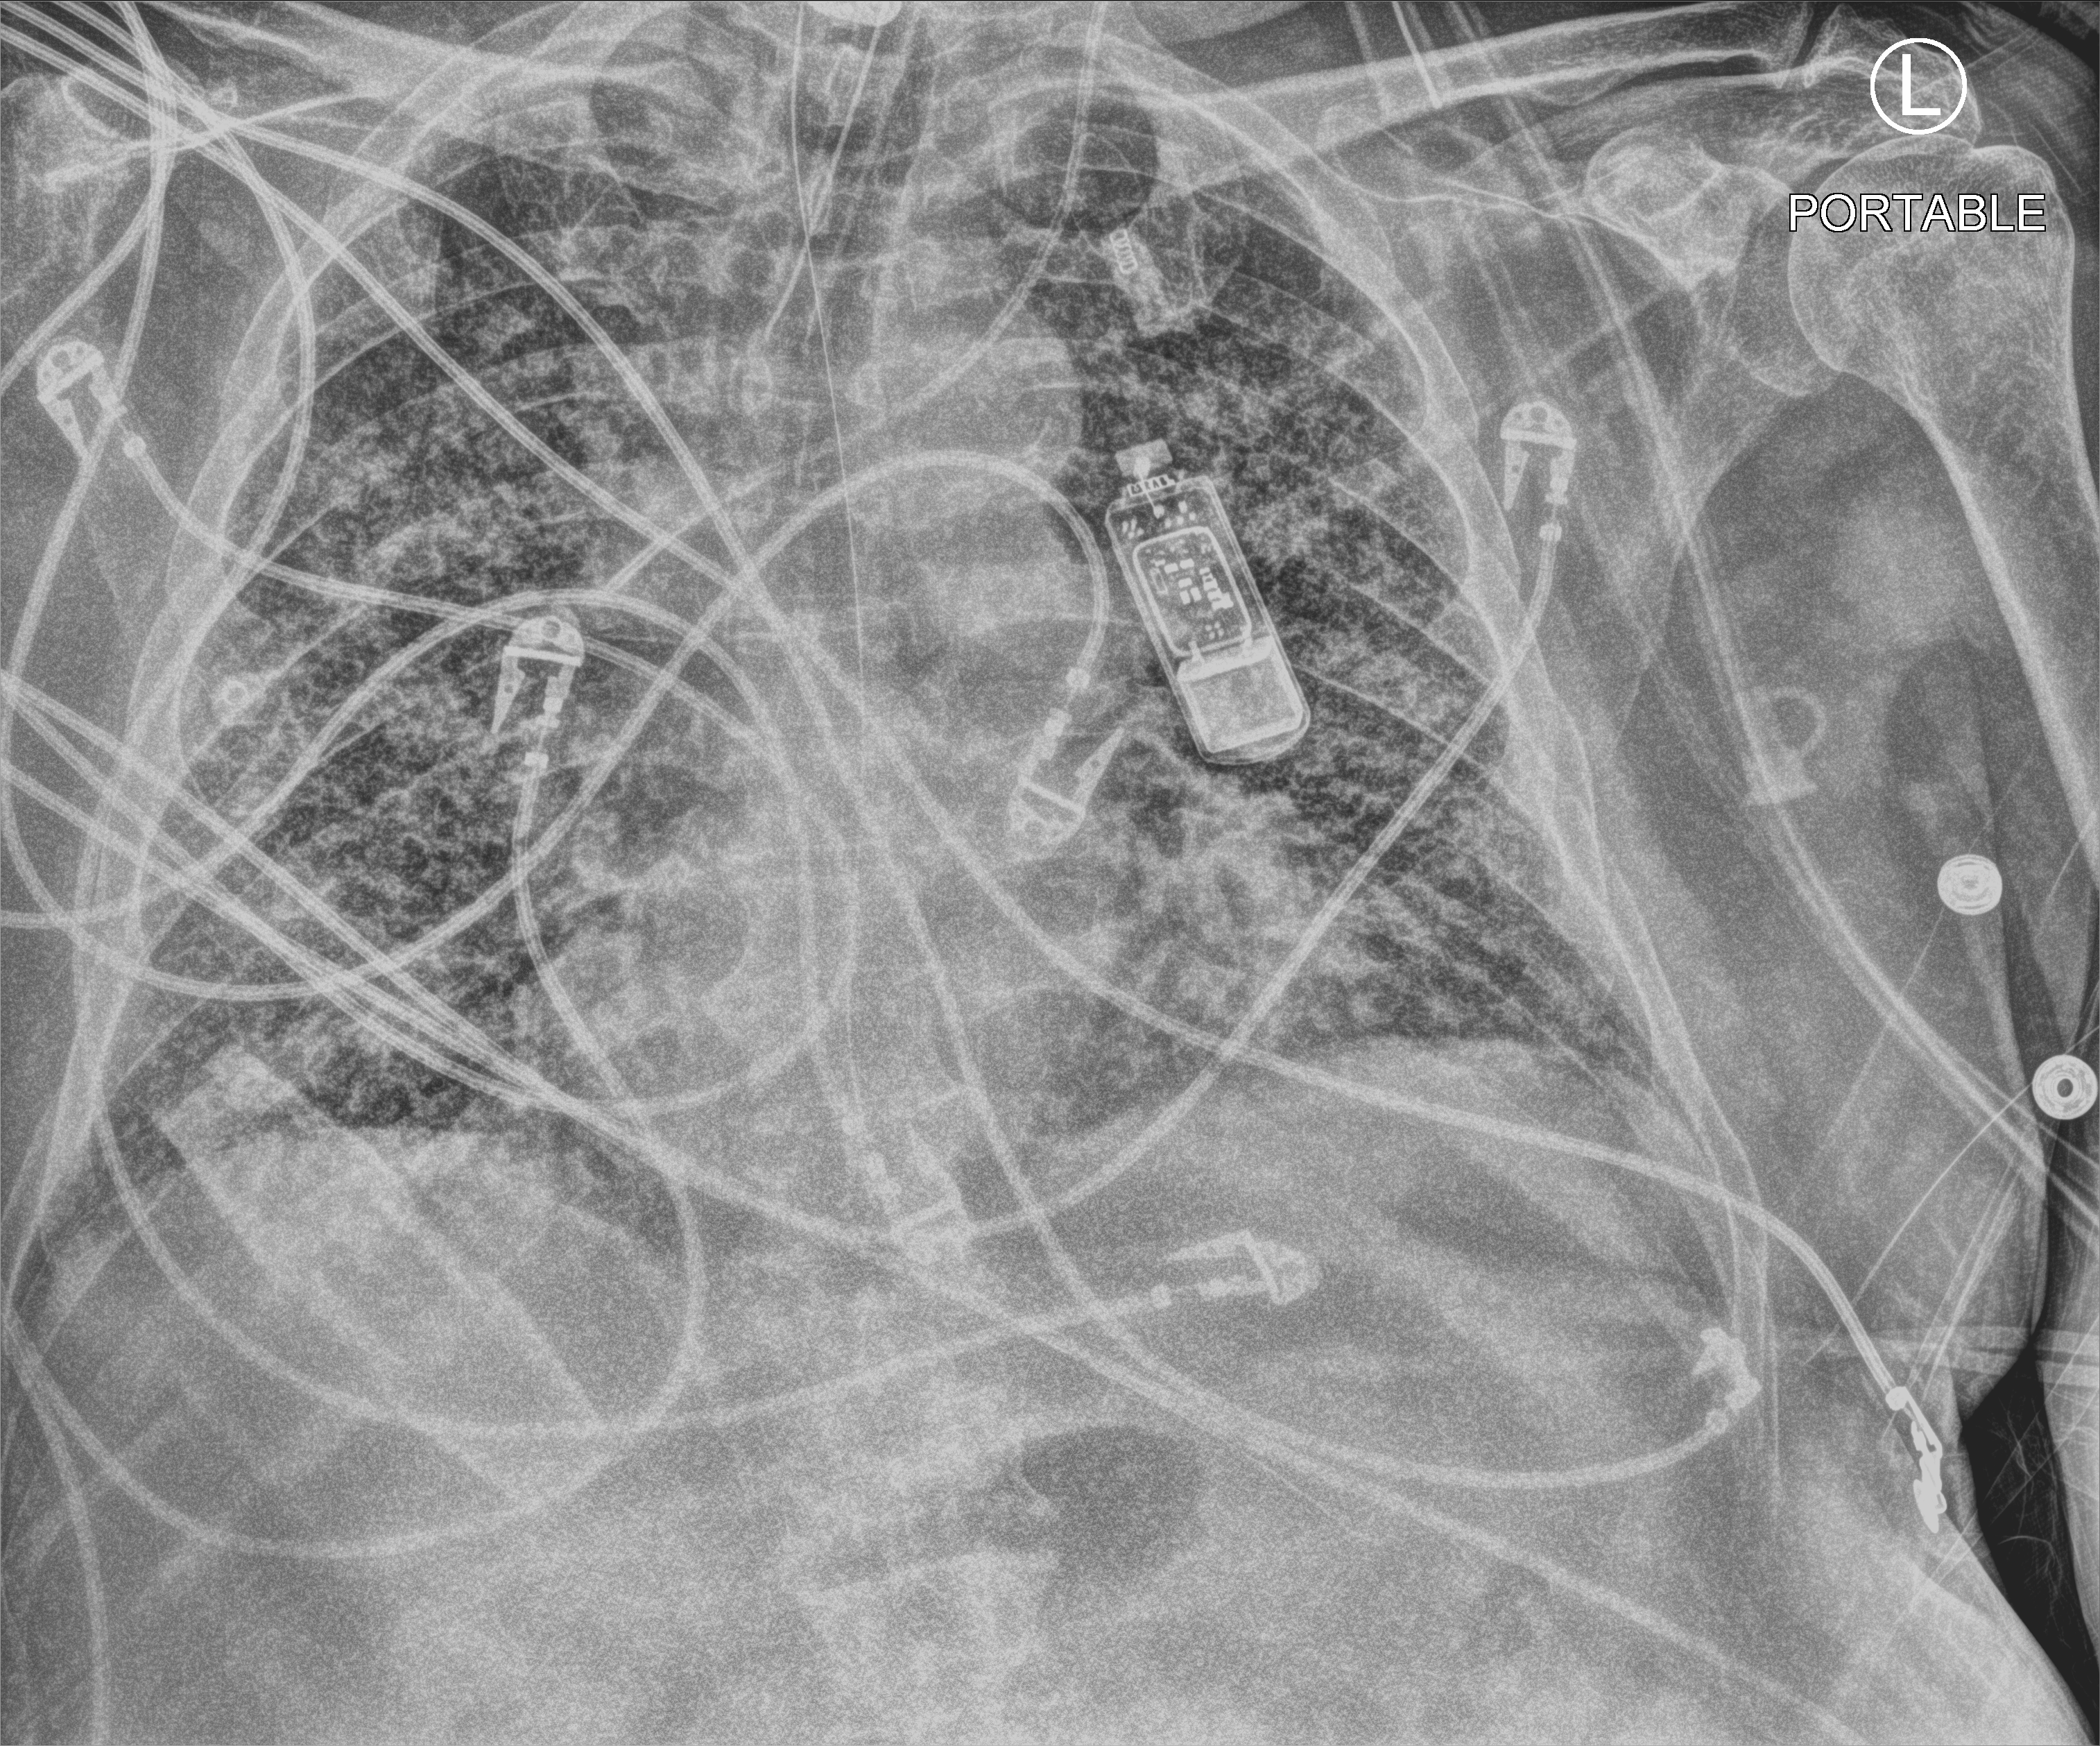
Bedside chest radiograph (computed radiography); anteroposterior (AP) projection. Patient hospitalised with COVID-19; male, aged 60–74 years.
Hospital-stay facts (about this admission, not read from this image; timing relative to this image not recorded): other chronic lung disease (admission record): yes.